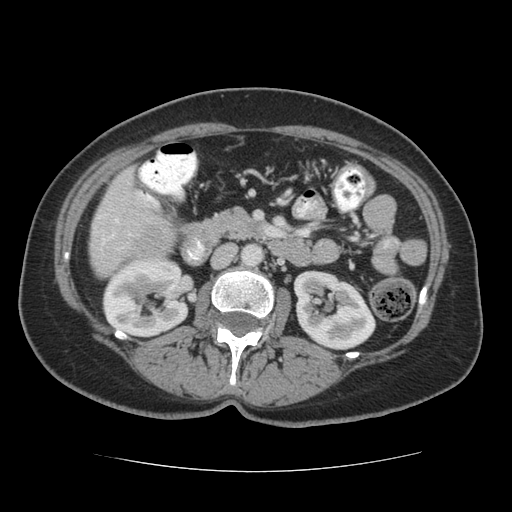
Contrast-enhanced abdominal CT (liver protocol), one axial slice. Position 14 of 75 along the scan axis. Reconstruction kernel STANDARD. 140 kVp. Soft-tissue window (W 400 / L 40 HU). 512 × 512 image matrix, field of view 360 × 360 mm. Case-level facts recorded for this patient, not image findings: diagnosis: hepatocellular carcinoma (patient treated with transarterial chemoembolisation; whether this scan precedes or follows treatment is not stated here); TNM stage (as recorded): Stage-I; Child-Pugh class: A; tumour nodularity: uninodular.
Outlined on this slice (semi-automatically segmented with operator editing):
- liver parenchyma outside the tumour (the mass and vessels are separate outlines, so this box may not span the whole liver): bounding box (x1, y1, x2, y2) in pixels: (90, 167, 174, 274)
- mass: (135, 223, 171, 259)
- liver vessels: (98, 192, 157, 250)